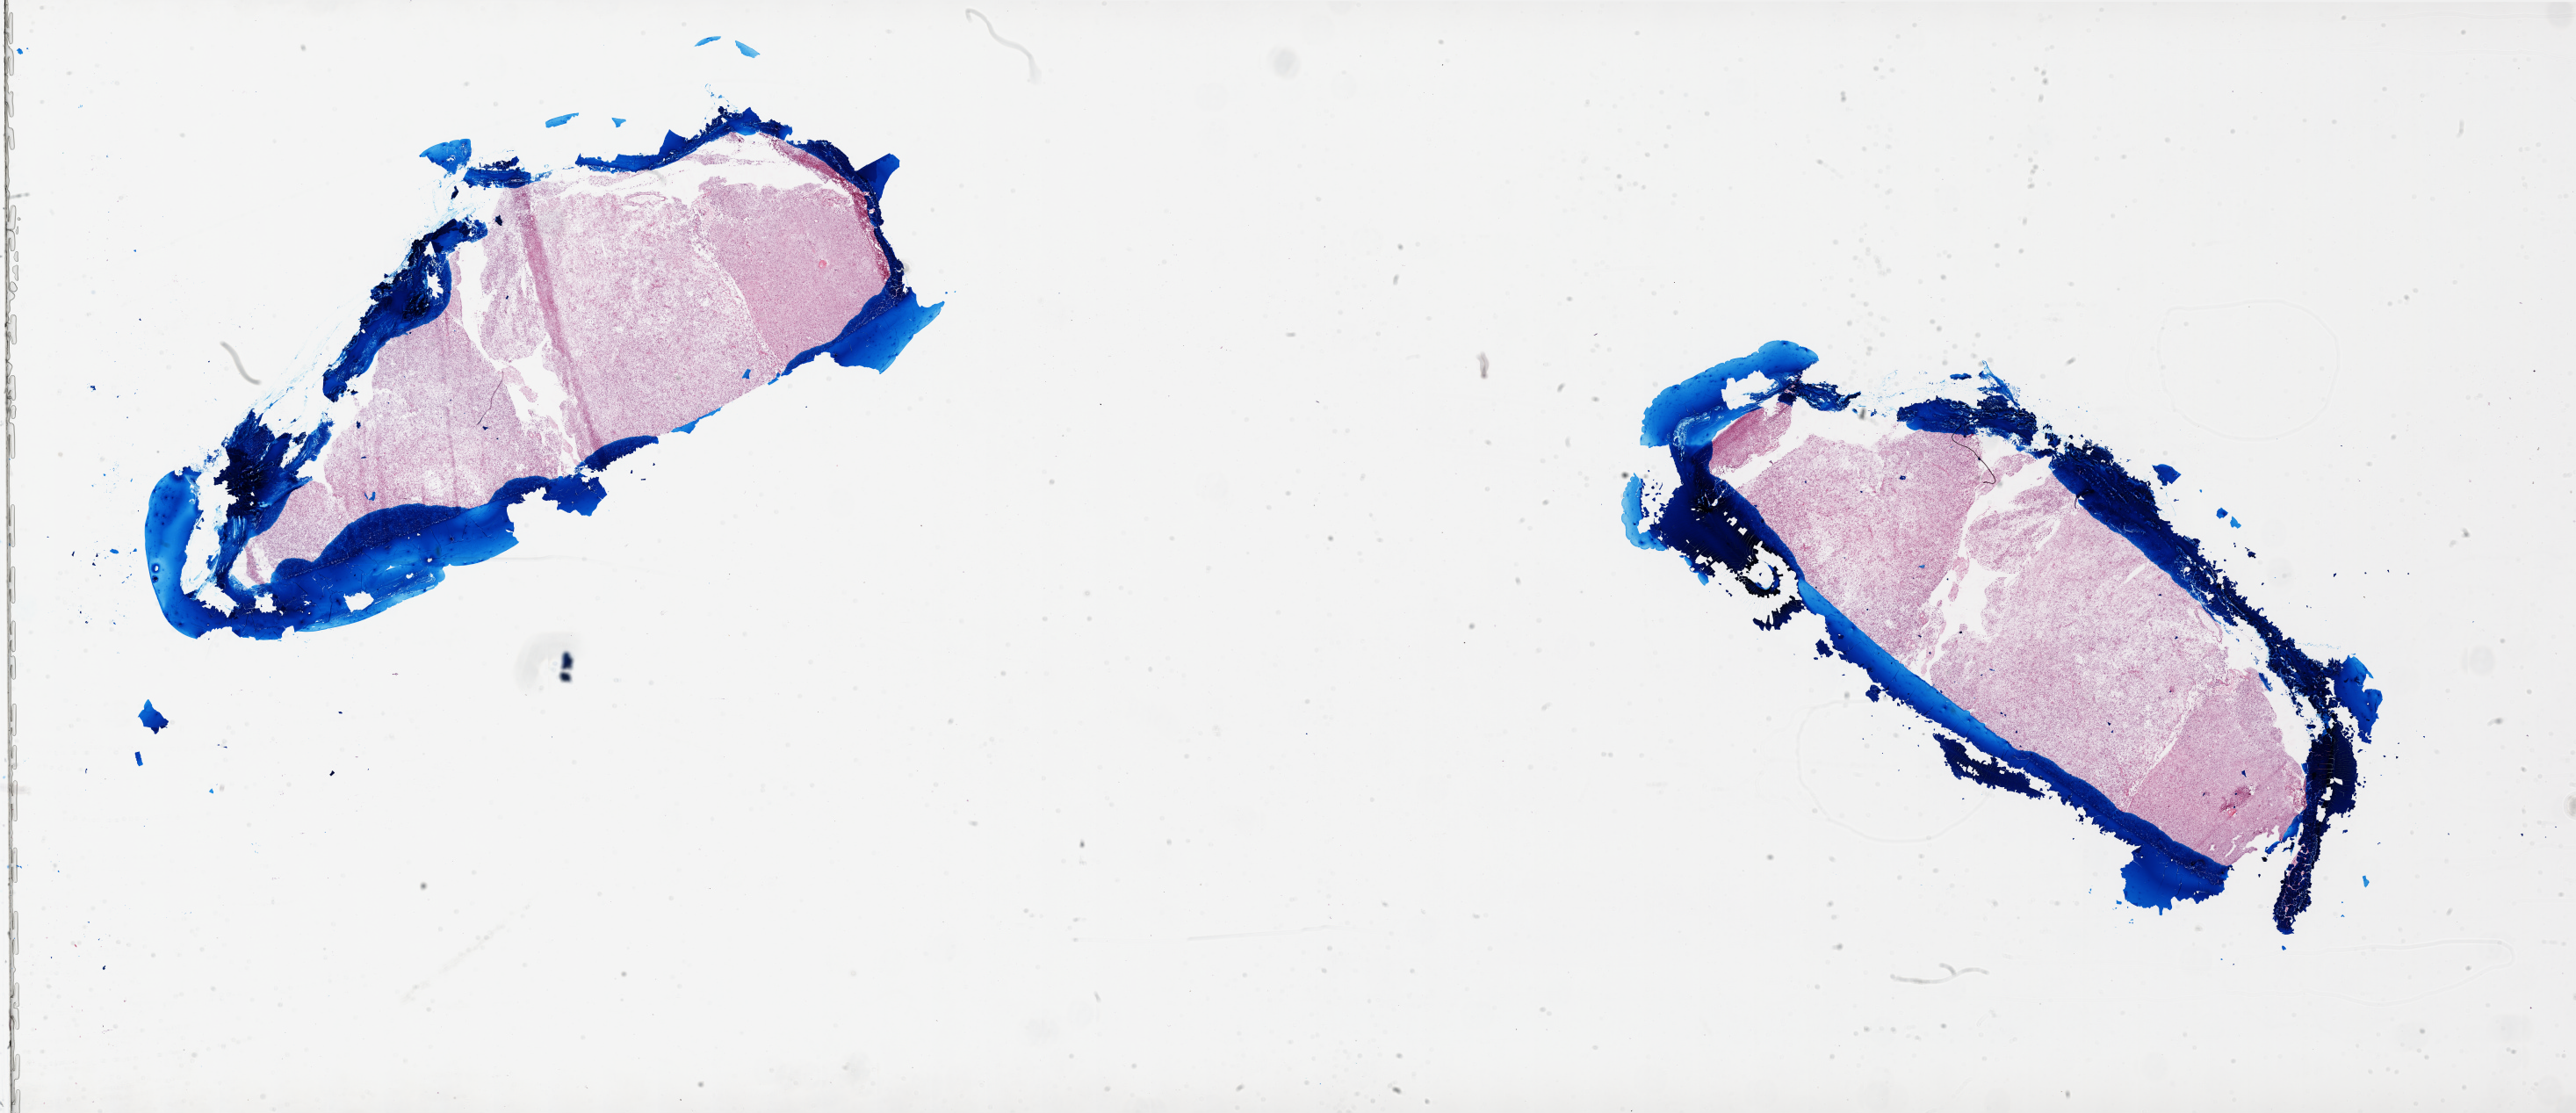
Whole-slide histology image, Hematoxylin and eosin (H&E) stained — low-resolution overview of the scanned area, about 47.0 x 20.3 mm (slide scanned at 20x); frozen section from the top of the tissue portion; brain, primary tumour sample. Male patient; age at initial diagnosis 35 years. Pathologist review of this section (percent, as recorded): tumour cells 80%, tumour nuclei 95%, normal cells 0%, stromal cells 20%, necrosis 5%.
* pathologic diagnosis: Glioblastoma